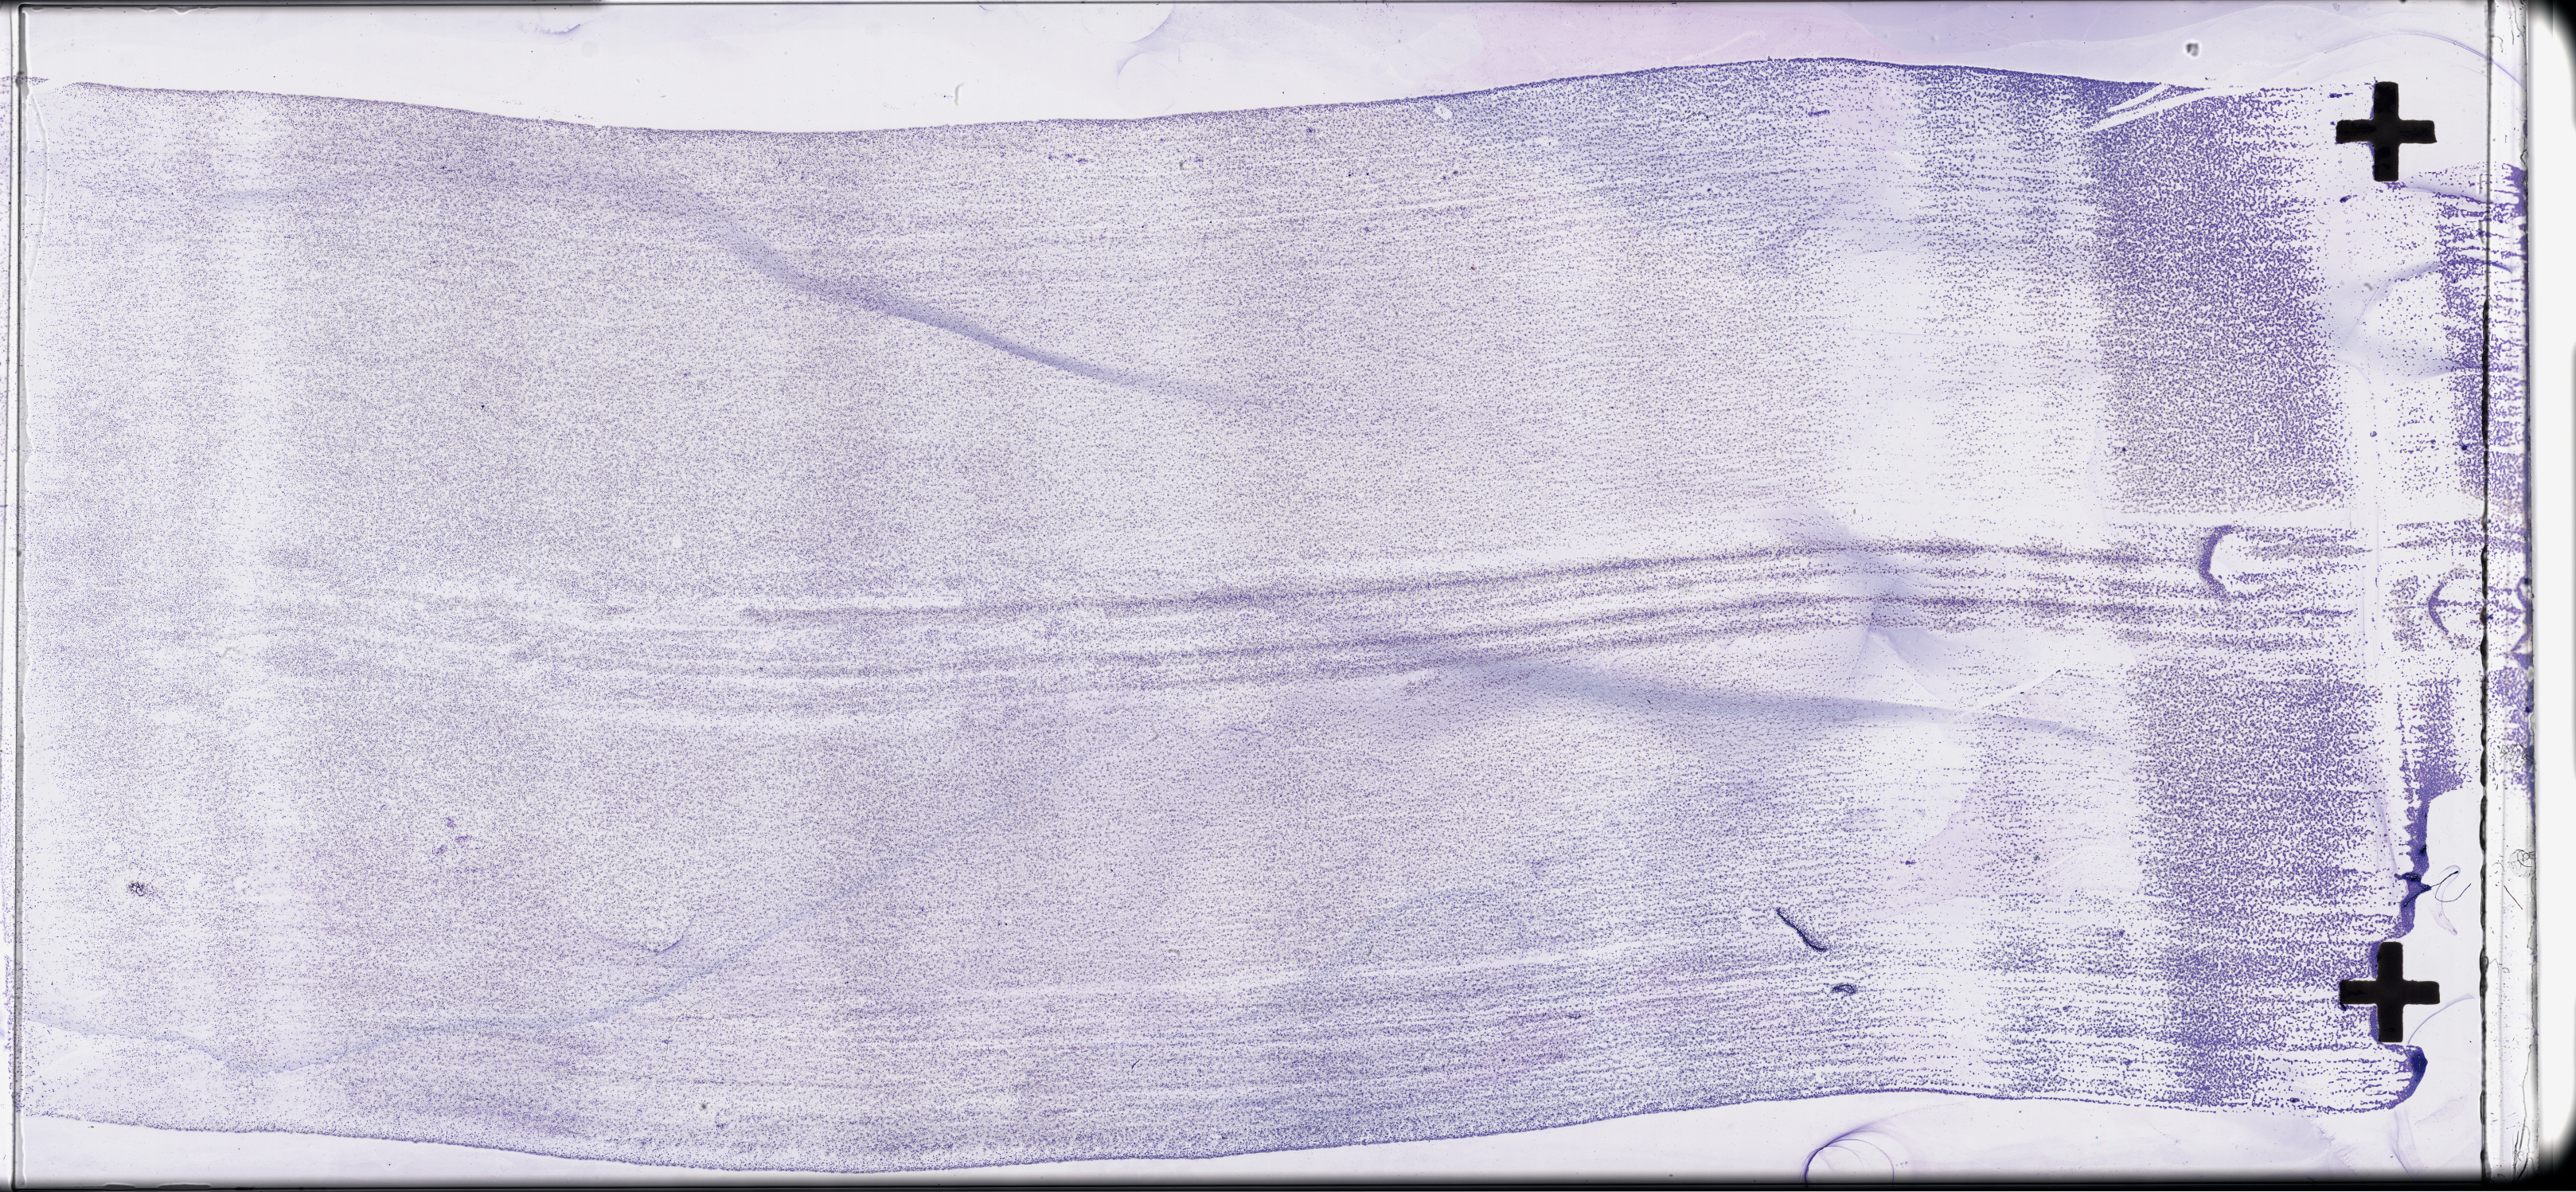
Digitized Hematoxylin and eosin (H&E) stained tissue section (whole slide), a low-resolution overview of the entire scanned area, about 52.3 x 24.2 mm; peripheral blood (leukaemic) sample. 70-year-old female patient.
FAB classification: M1. Diagnosis: Acute Myeloid Leukemia.